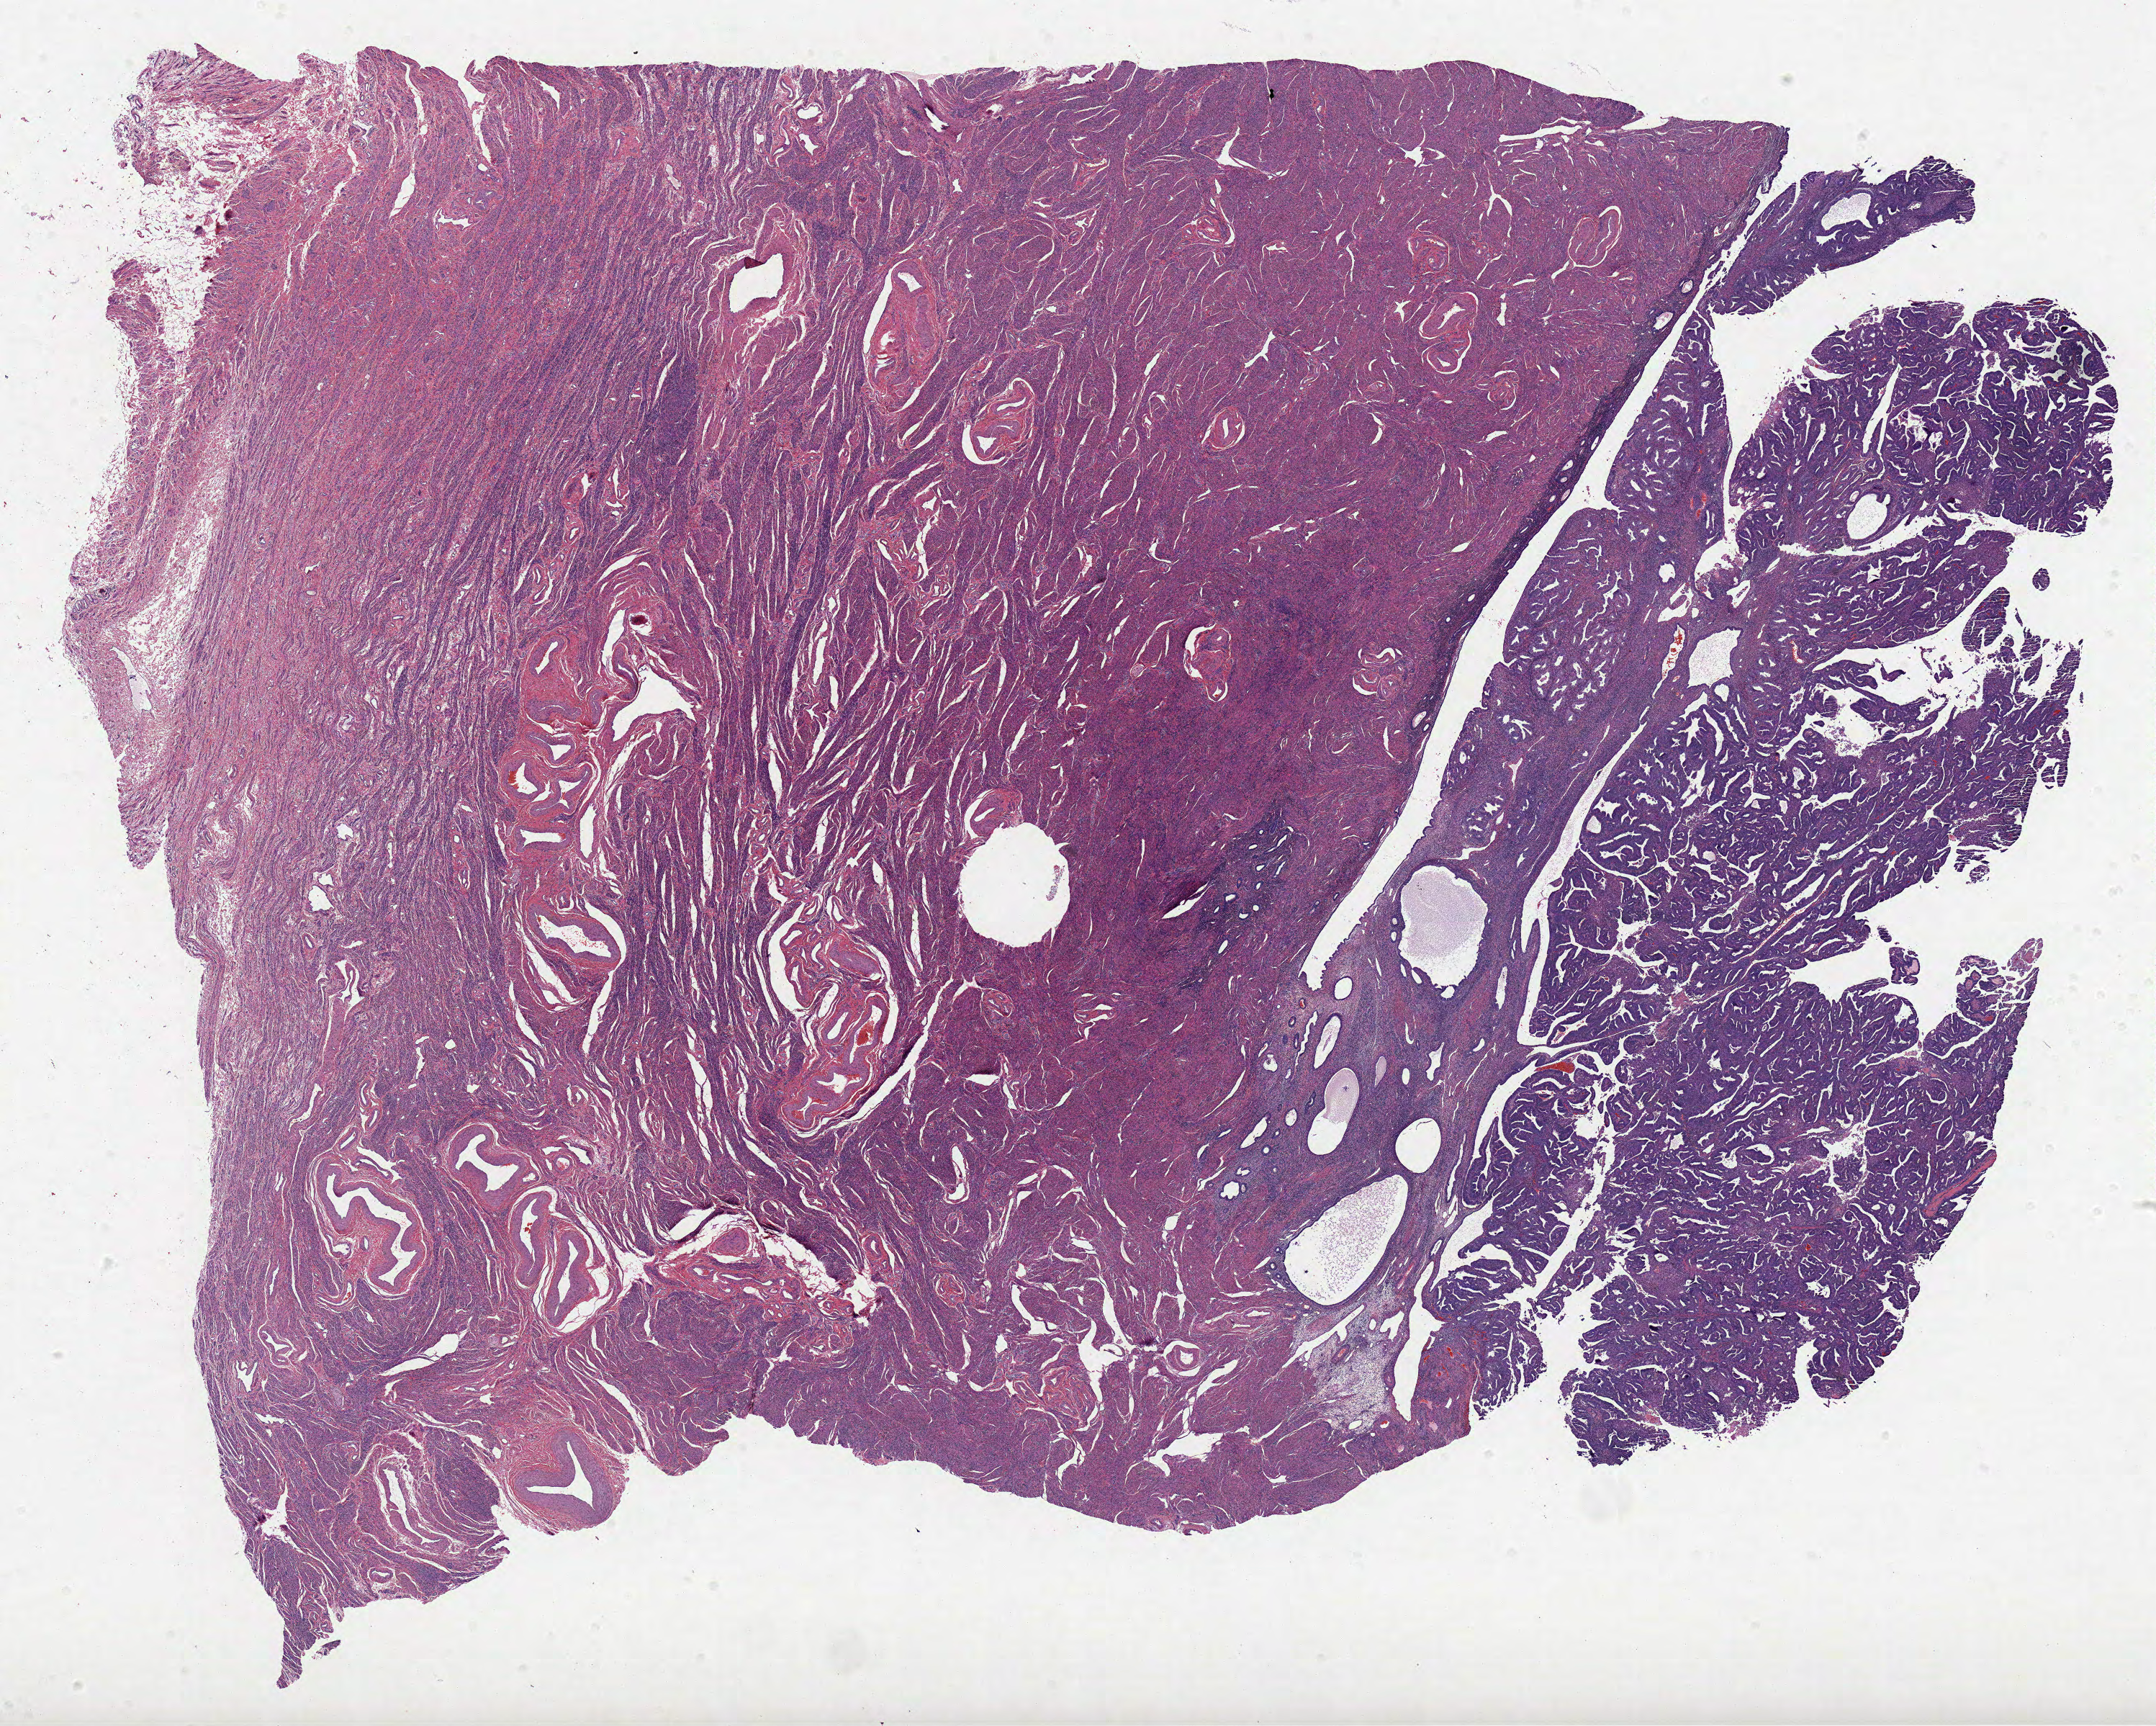
H&E whole-slide image — whole scanned area (about 23.9 x 19.1 mm, from a 20x scan) shown as a low-resolution overview. Formalin-fixed paraffin-embedded (FFPE) diagnostic section. Sample: primary tumour, uterus. Female, age 56 years at initial diagnosis.
Histologic diagnosis: Endometrioid adenocarcinoma, NOS (endometrium).